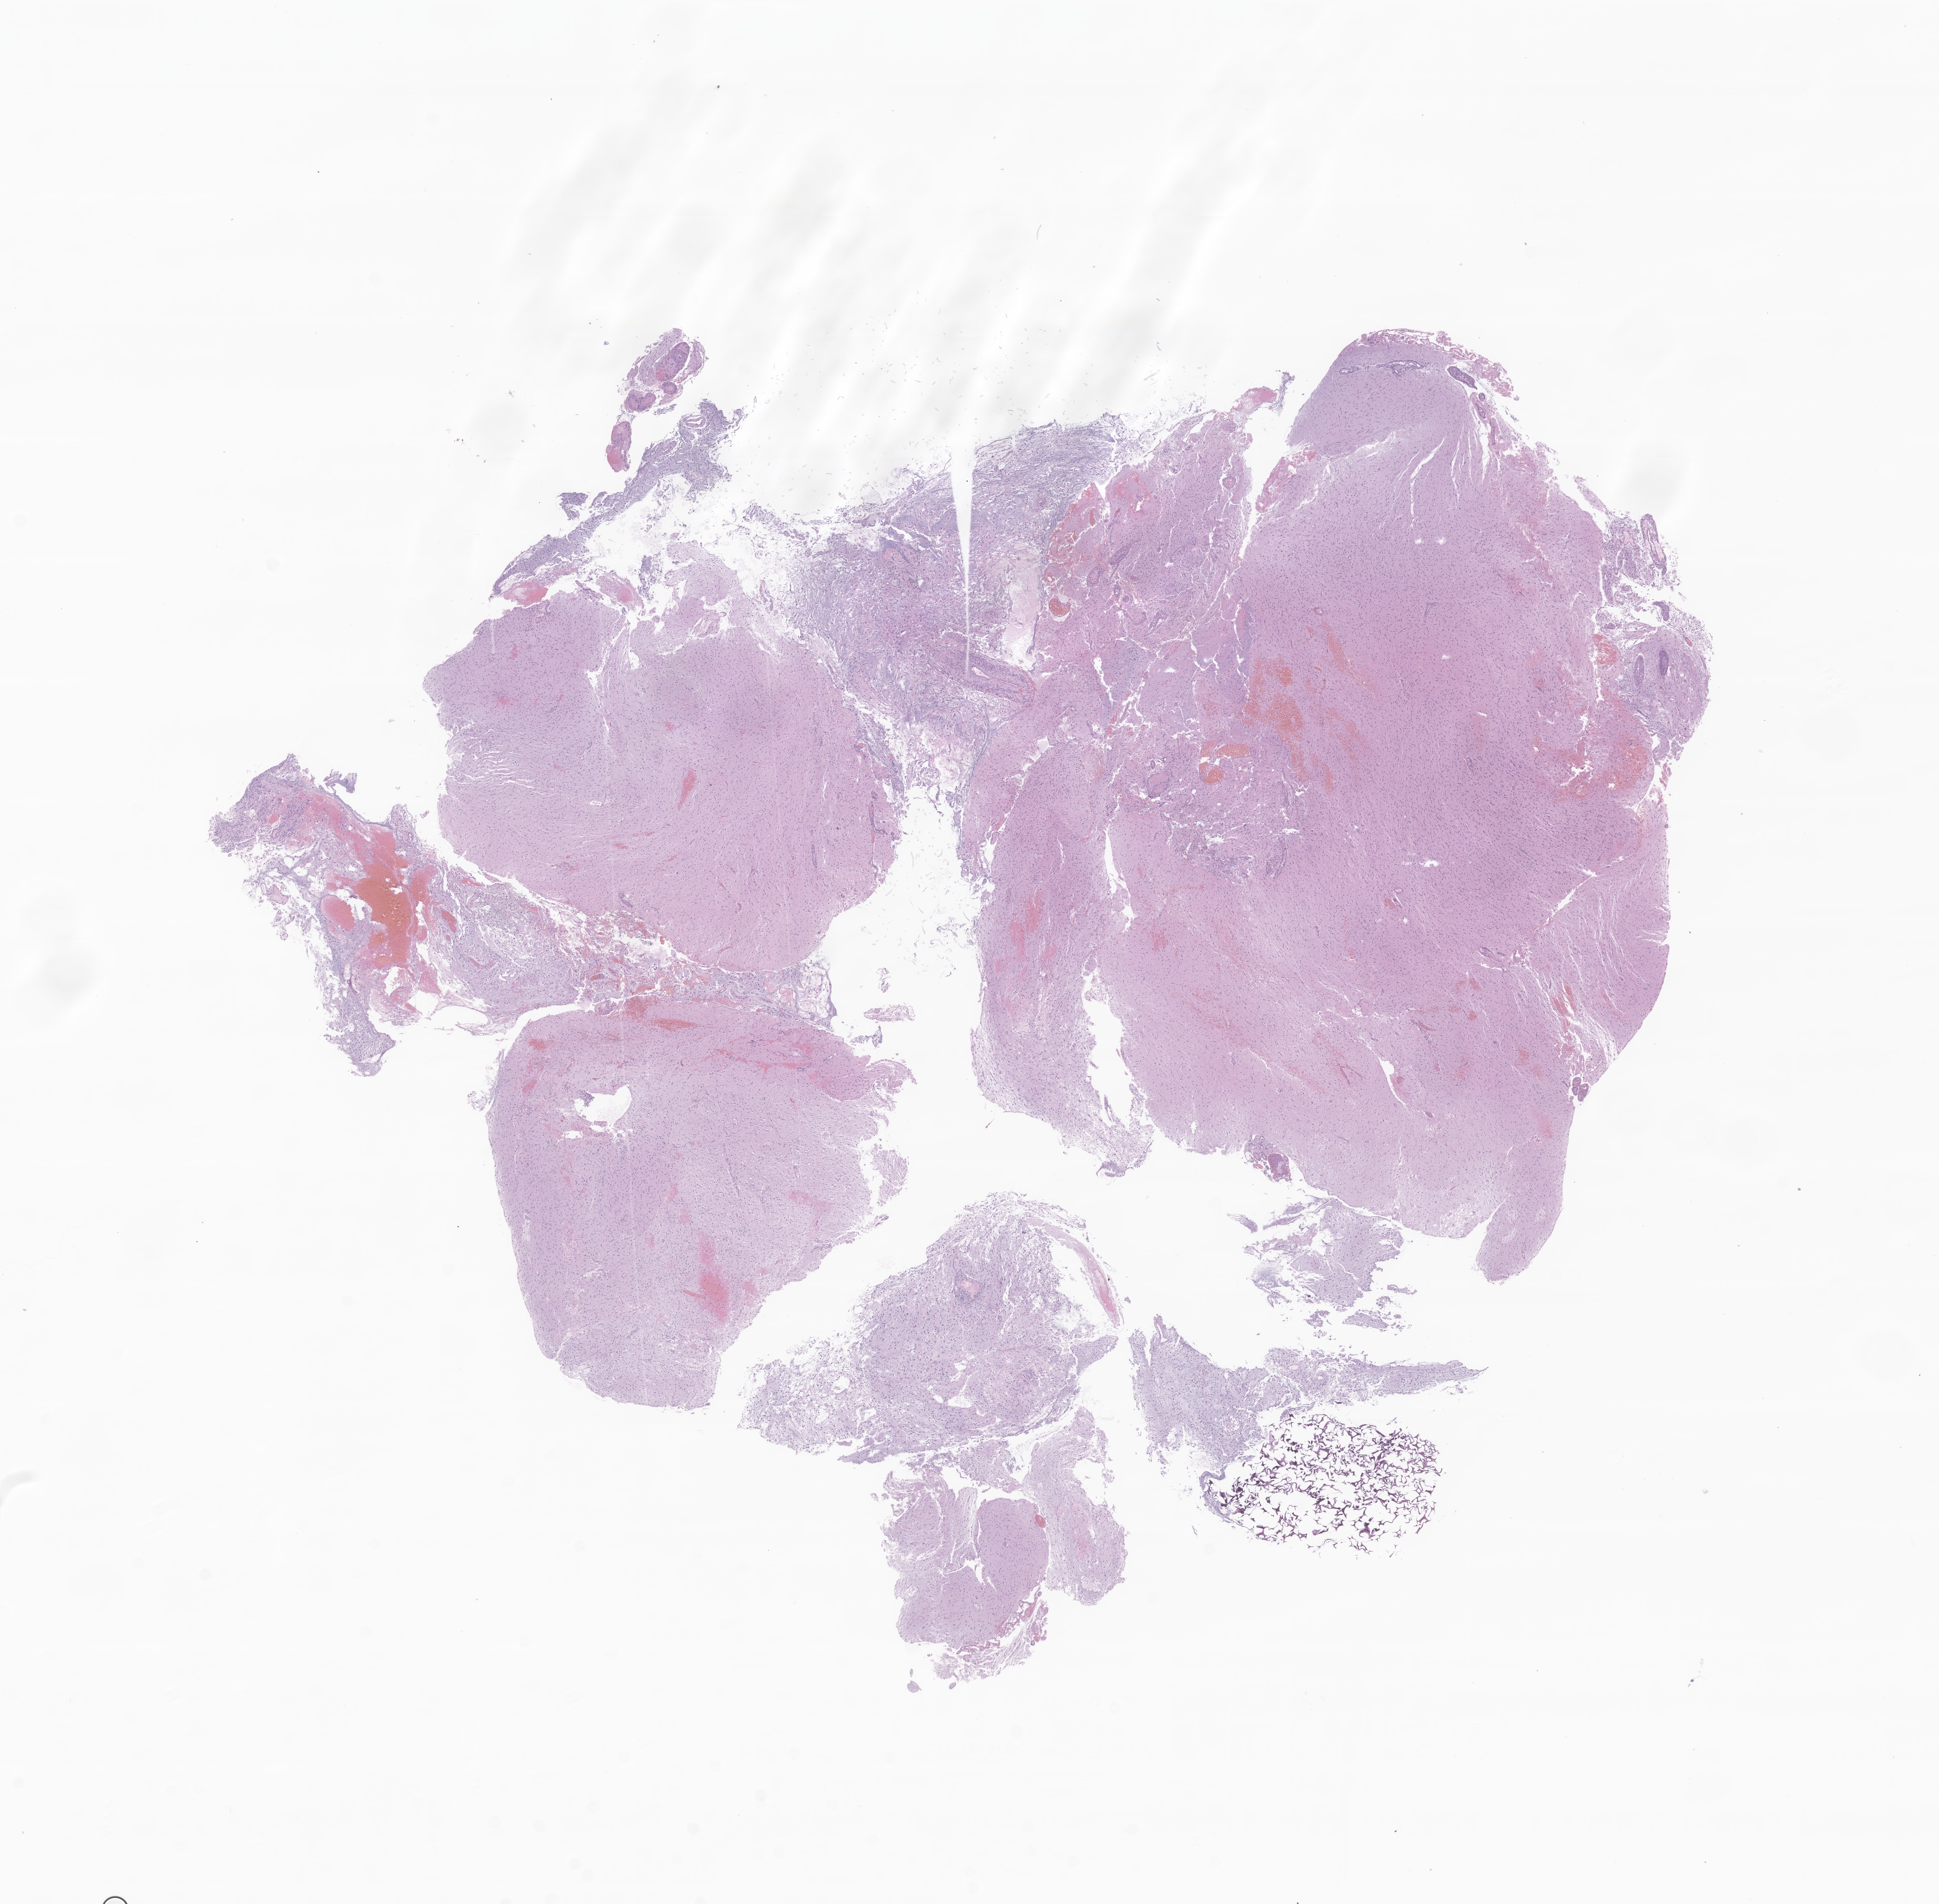
Digitized hematoxylin and eosin (H&E)-stained section of tumor tissue from the cerebrum — a low-resolution overview of the entire scanned area, about 17.1 x 16.8 mm, formalin-fixed, paraffin-embedded (FFPE) tissue. Patient: male, age 127 months (10 years 7 months).
Recorded diagnosis: Pilocytic astrocytoma.